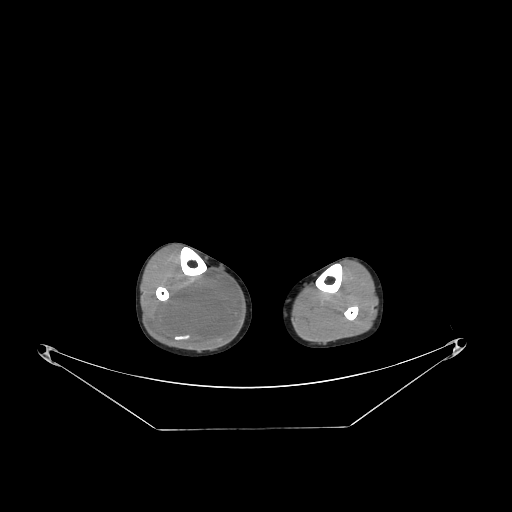
CT of an extremity soft-tissue mass (from a PET/CT study), one axial slice; slice 96 of 267 in the series (ordered by position); reconstruction kernel STANDARD; soft-tissue window (W 400 / L 40 HU); 3.75 mm slice thickness; 512 × 512 image matrix. Male patient. Case-level facts recorded for this patient, not image findings: histological type: liposarcoma - round cell; grade: high; site of the primary tumour: right calf.
Outlined on this slice (expert contour drawn on MRI and transferred to this co-registered scan by the dataset authors):
- gross tumour volume (mass): bounding box (x1, y1, x2, y2) in pixels: (151, 270, 241, 350)